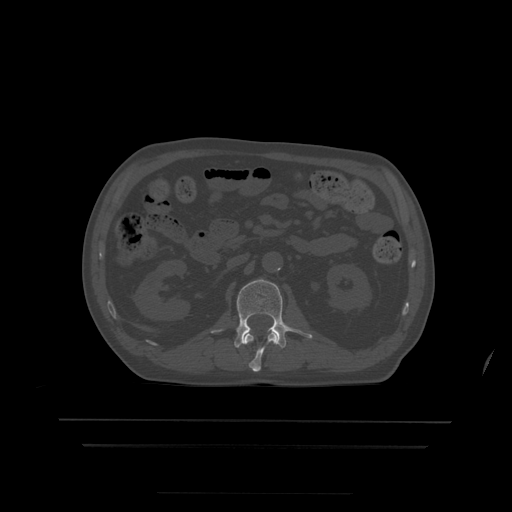
CT including the spine, one axial slice; slice 153 of 522 in the series (ordered by position); bone window (W 1800 / L 400 HU); 1.25 mm slice thickness; 512 × 512 image matrix, field of view 436 × 436 mm. Patient age 68 years. From the clinical record (not read from this slice): primary cancer: urothelial.
Structures marked on this image (semi-automatically segmented with operator editing):
- L1 vertebra: bounding box <245,333,278,372> (left, top, right, bottom; pixels)
- L2 vertebra: <212,280,313,349>